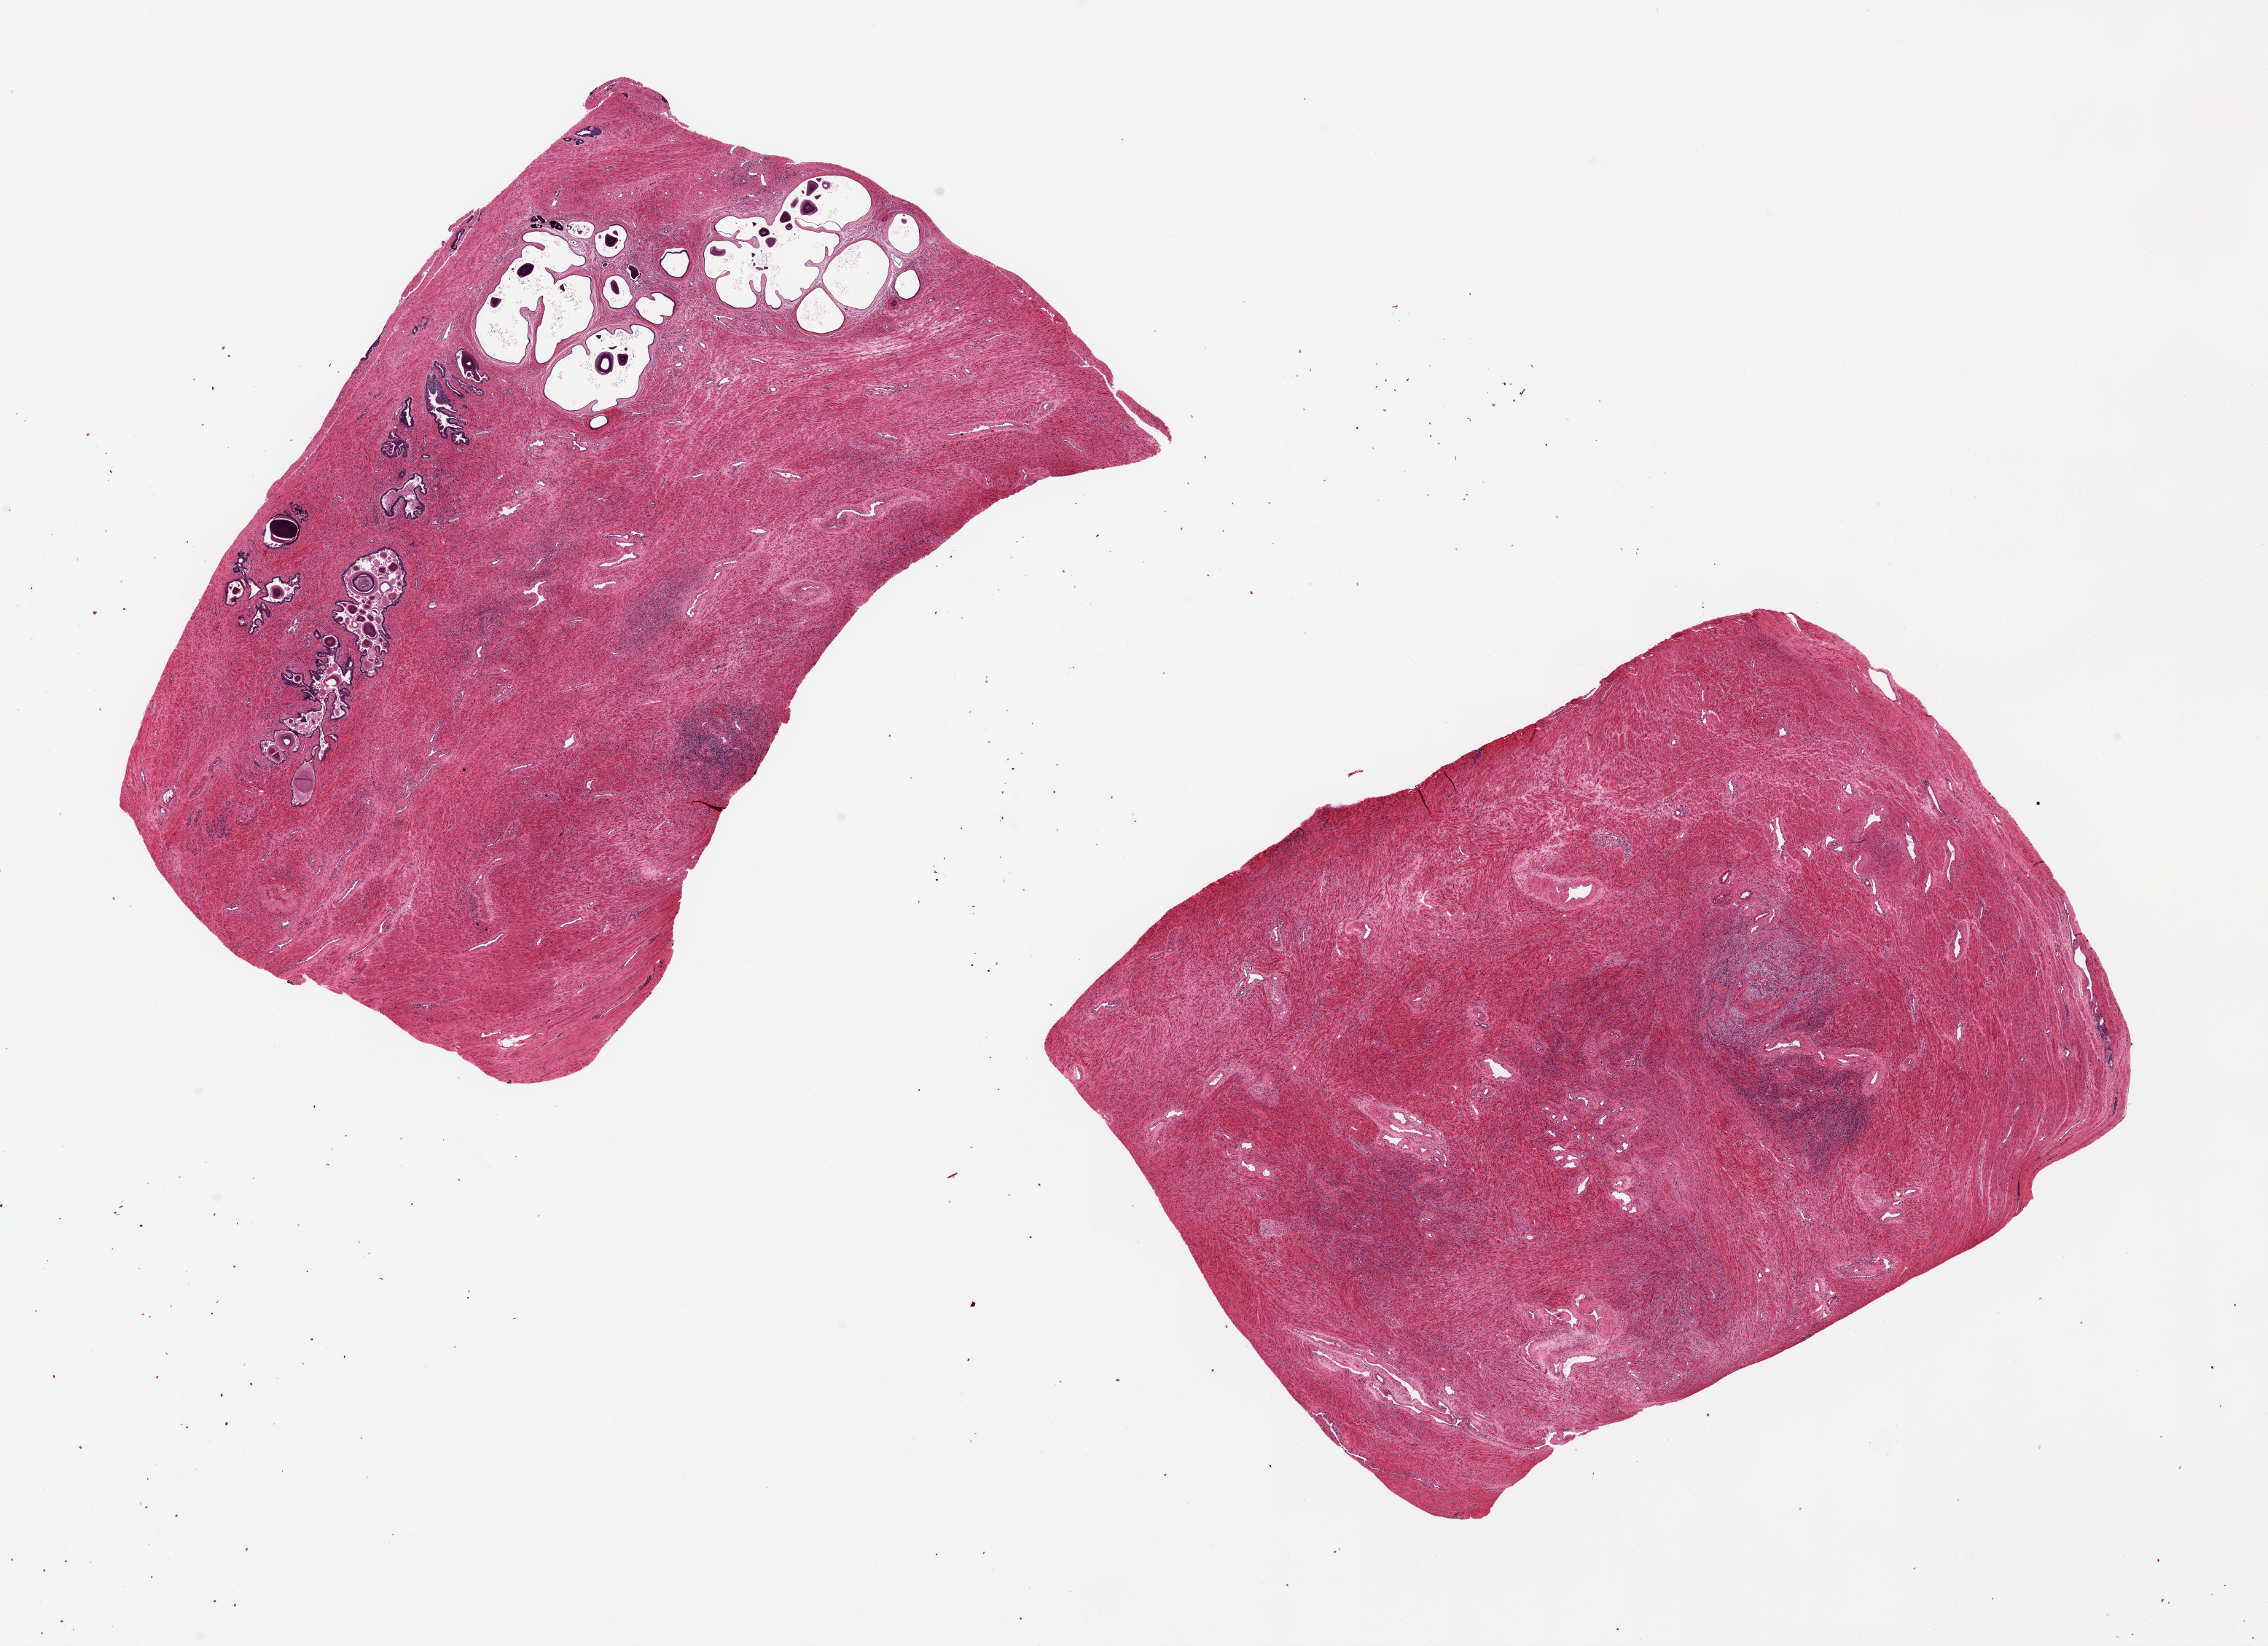
Digitized hematoxylin and eosin (H&E)-stained section, low-resolution overview of the scanned area, about 24.6 x 17.9 mm (acquisition: 20x scan). PAXgene-fixed, paraffin-embedded tissue. Section of prostate (target tissue). Donor tissue sample. Donor: male.
Pathologist's review note for this sample: 2 ~ 9x6mm pieces, one with stromal hyperplasia devoid of glands, the other with seminal vesicle.